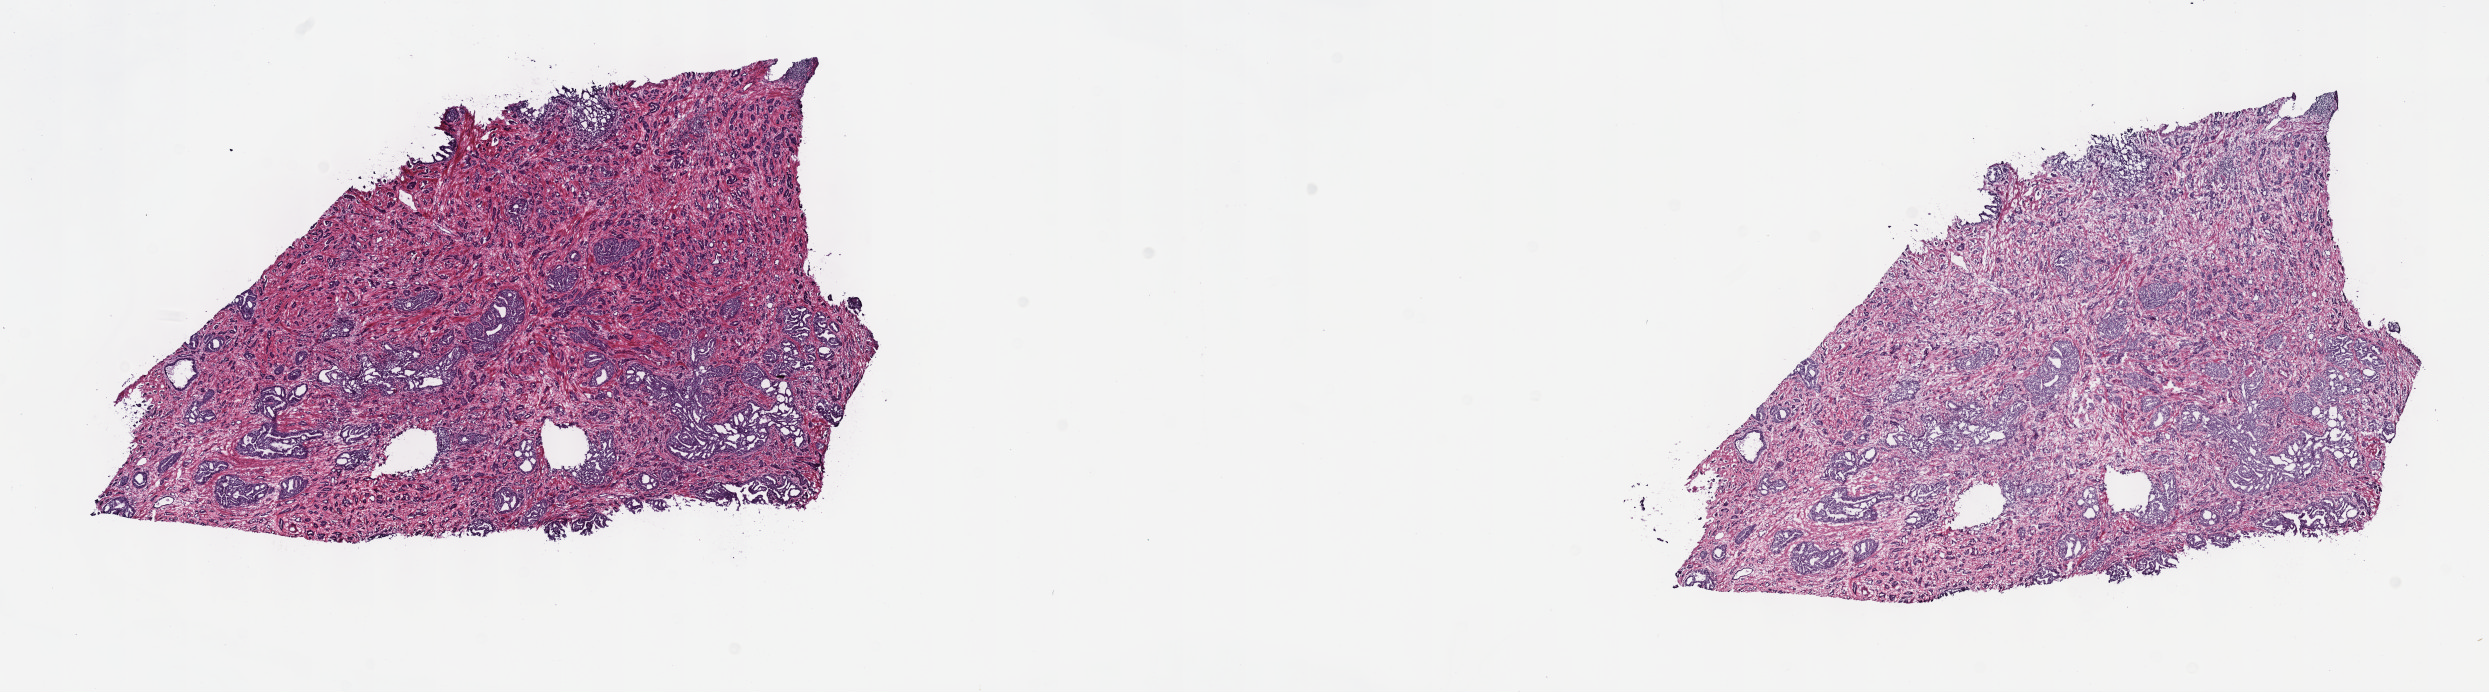
H&E-stained whole-slide image — a low-resolution overview of the entire scanned area, about 20.1 x 5.6 mm; frozen section from the top of the tissue portion; prostate, primary tumour sample. Male patient; age at initial diagnosis 69 years. Slide review estimates, as recorded: tumour cells 80%, tumour nuclei 80%.
Diagnosis: Adenocarcinoma, NOS.